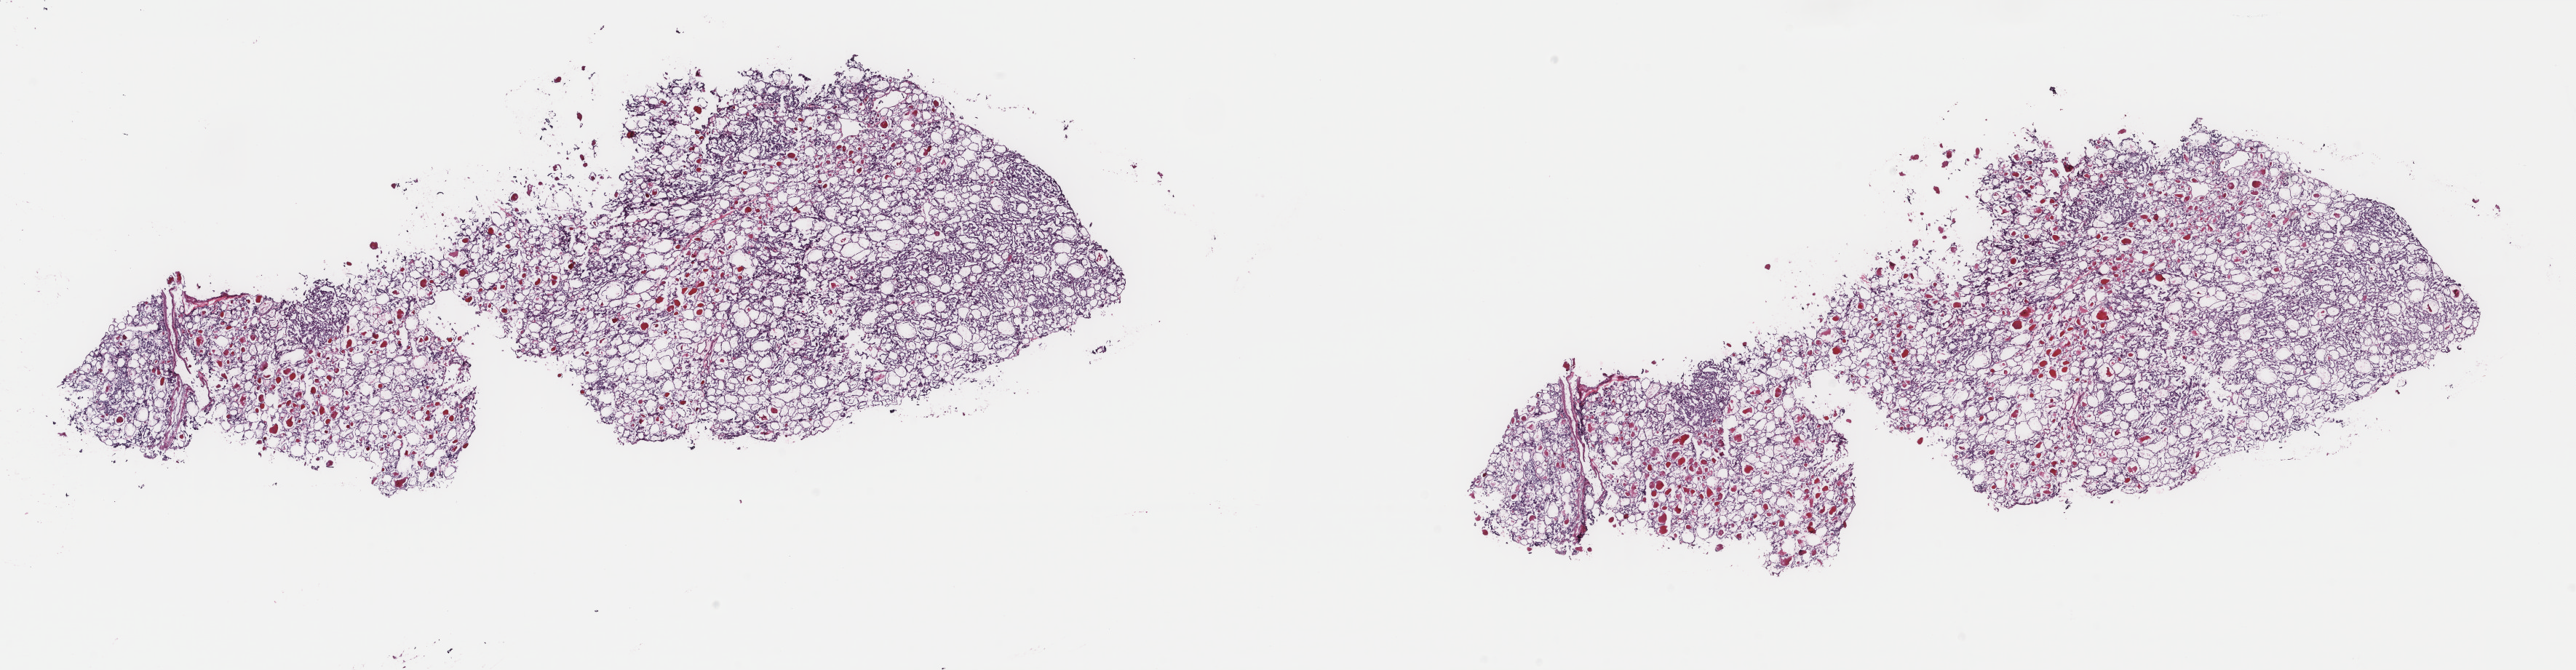
Whole-slide histology image, H&E, low-resolution overview of the scanned area, about 28.1 x 7.3 mm (acquisition: 40x scan); frozen section from the top of the tissue portion; thyroid, primary tumour sample. Female, age 70 years at initial diagnosis. Slide review estimates, as recorded: tumour cells 90%, tumour nuclei 100%, normal cells 0%, stromal cells 10%, necrosis 0%. Infiltration values recorded for this section: lymphocyte infiltration 0%, monocyte infiltration 0%, neutrophil infiltration 0%.
- AJCC pathologic stage: II (7th edition)
- laterality: left
- TNM: T2 N0 M0
- pathologic diagnosis: Papillary adenocarcinoma, NOS